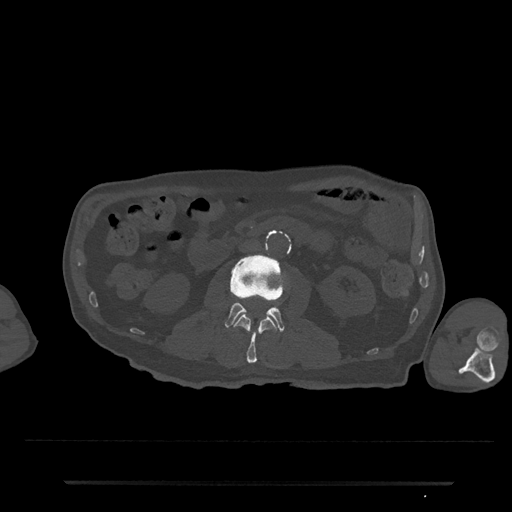
CT including the spine, one axial slice; position 22 of 797 along the scan axis; 120 kVp; bone window (W 1800 / L 400 HU); 0.5 mm slice thickness; 512 × 512 image matrix, field of view 427 × 427 mm. Male patient, age 74 years. From the clinical record (not read from this slice): primary cancer: prostate.
Structures marked on this image (semi-automatic segmentation, software-assisted and operator-edited):
- L2 vertebra: box from (x=234, y=314) to (x=277, y=364) px
- L3 vertebra: (x=225, y=255)–(x=285, y=332)